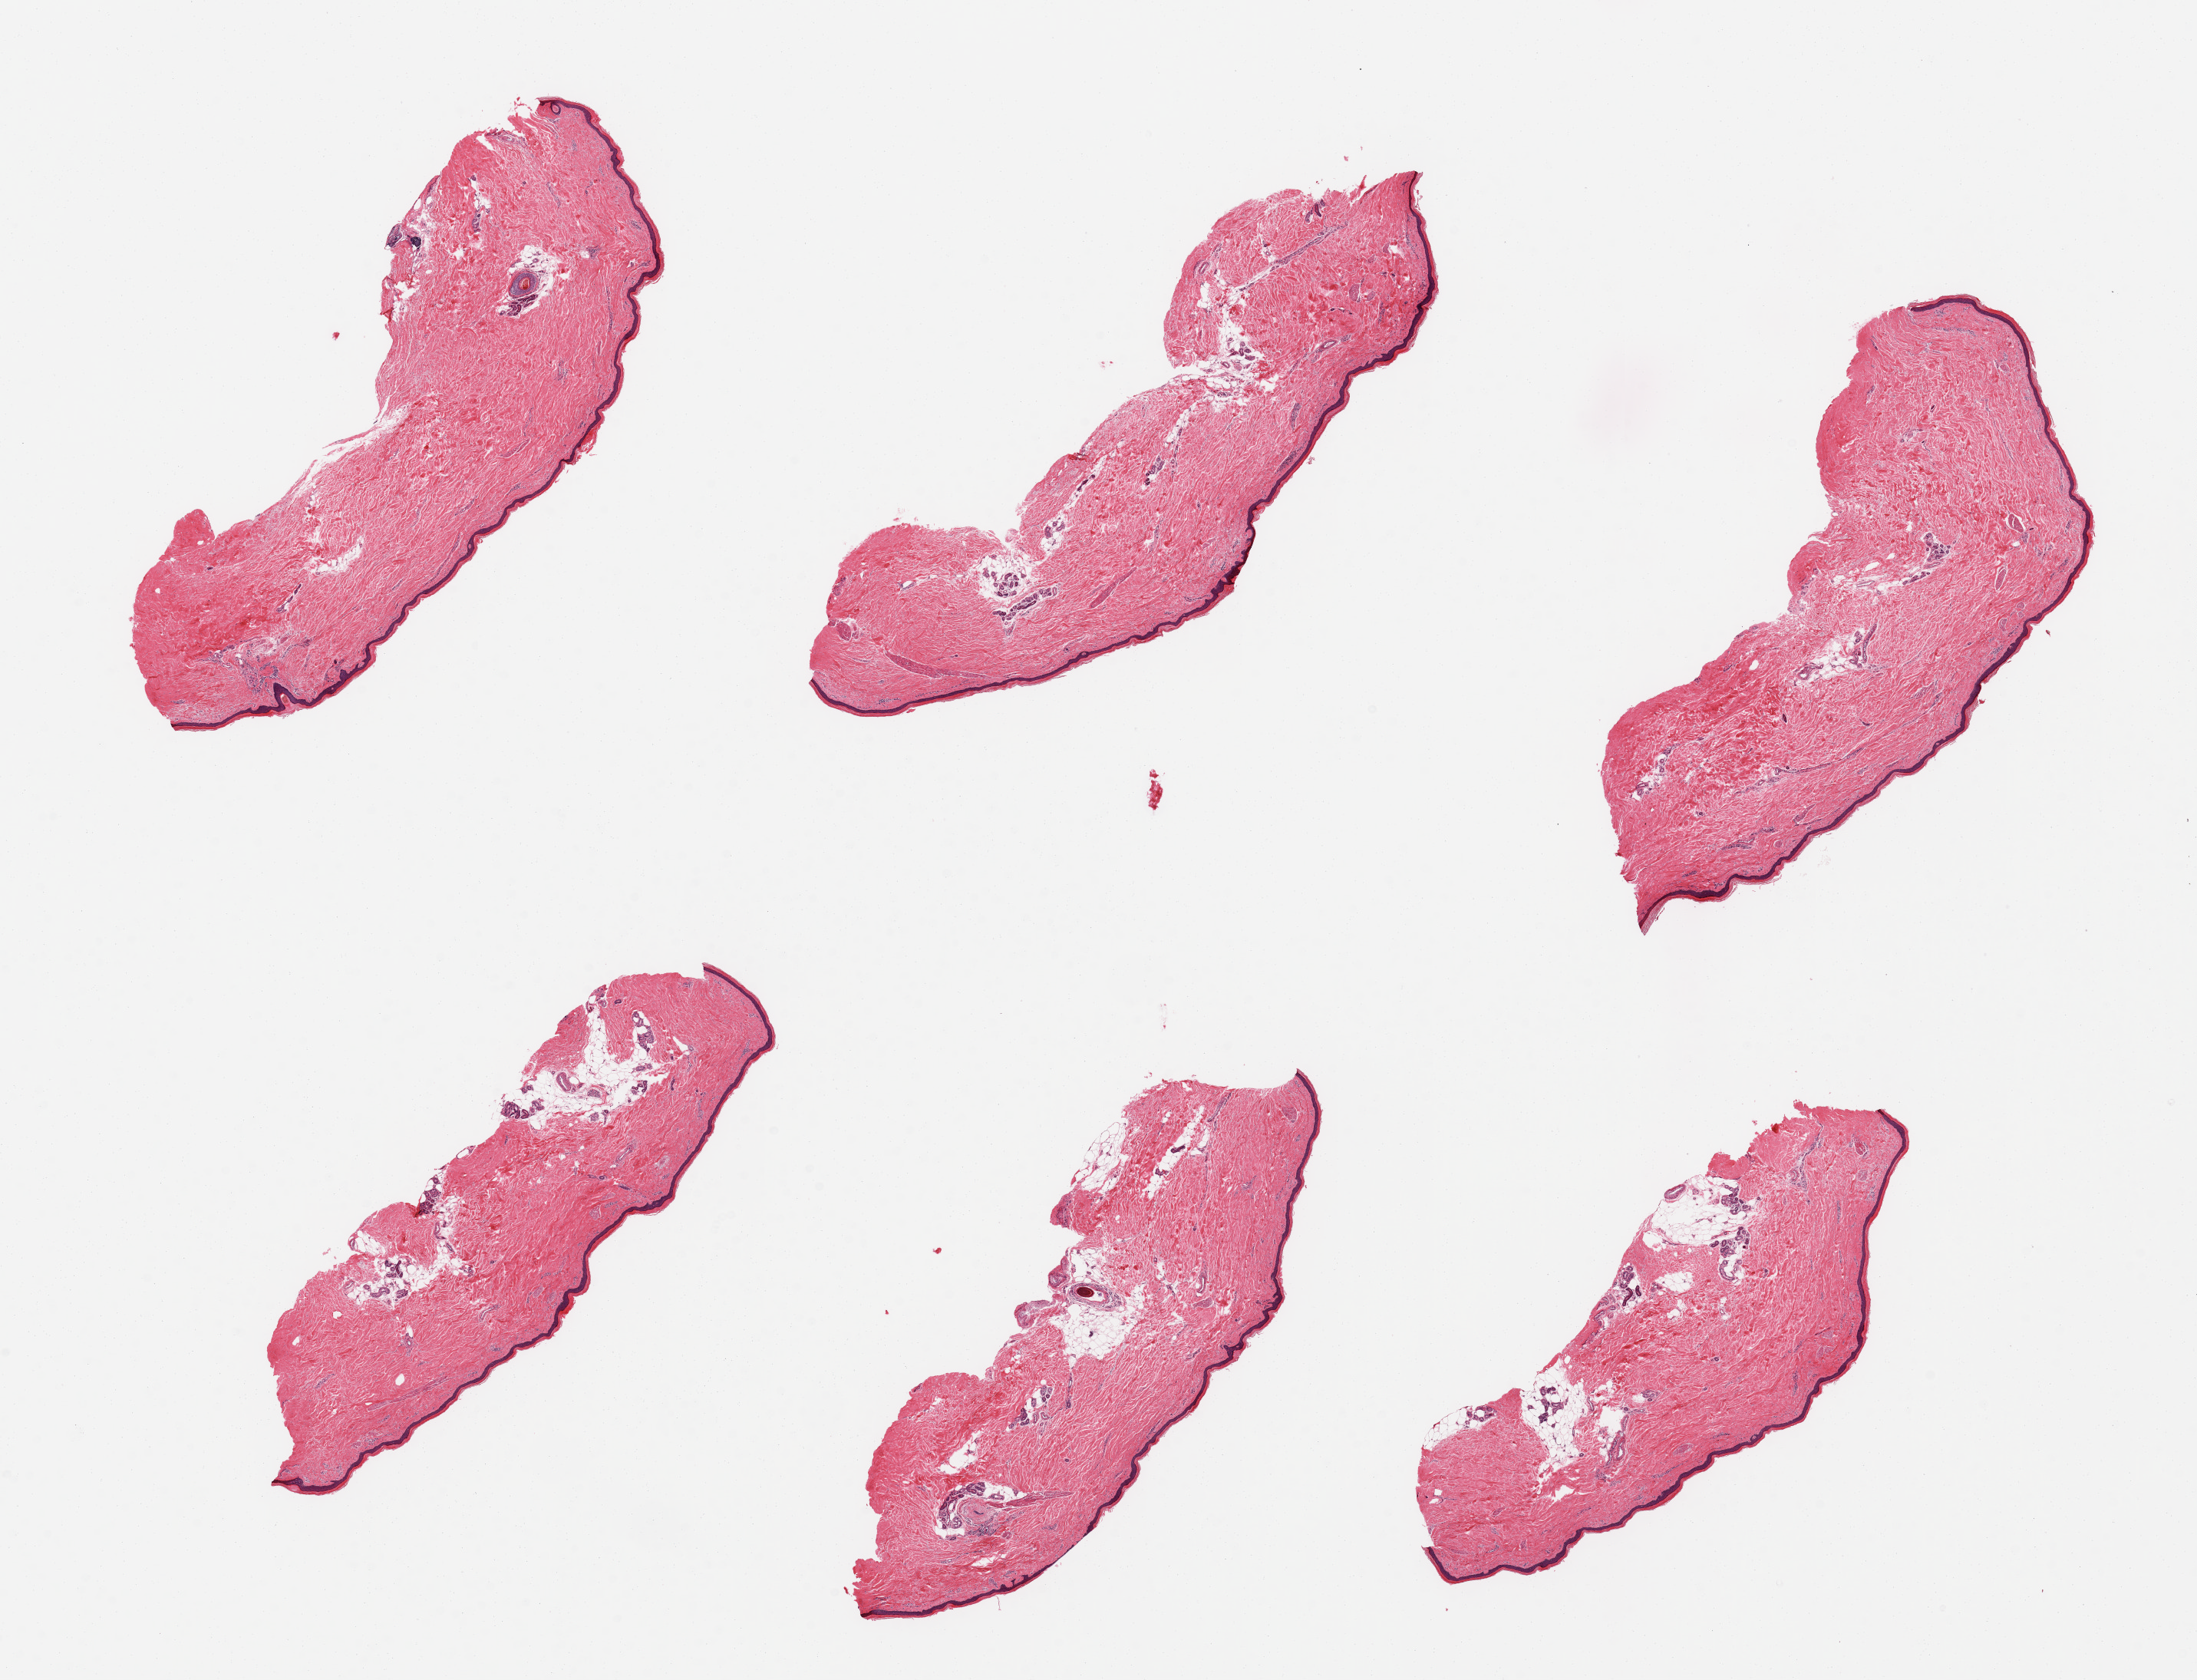
Digitized hematoxylin and eosin (H&E)-stained section — a low-resolution overview of the entire scanned area, about 22.6 x 17.3 mm, PAXgene-fixed, paraffin-embedded tissue, sampled site (target tissue): skin of lower leg, tissue donor sample. Donor: male.
Pathologist's review note for this sample: 6 pieces, minimal dermal fat, squamous epithelium is 25-40 microns.